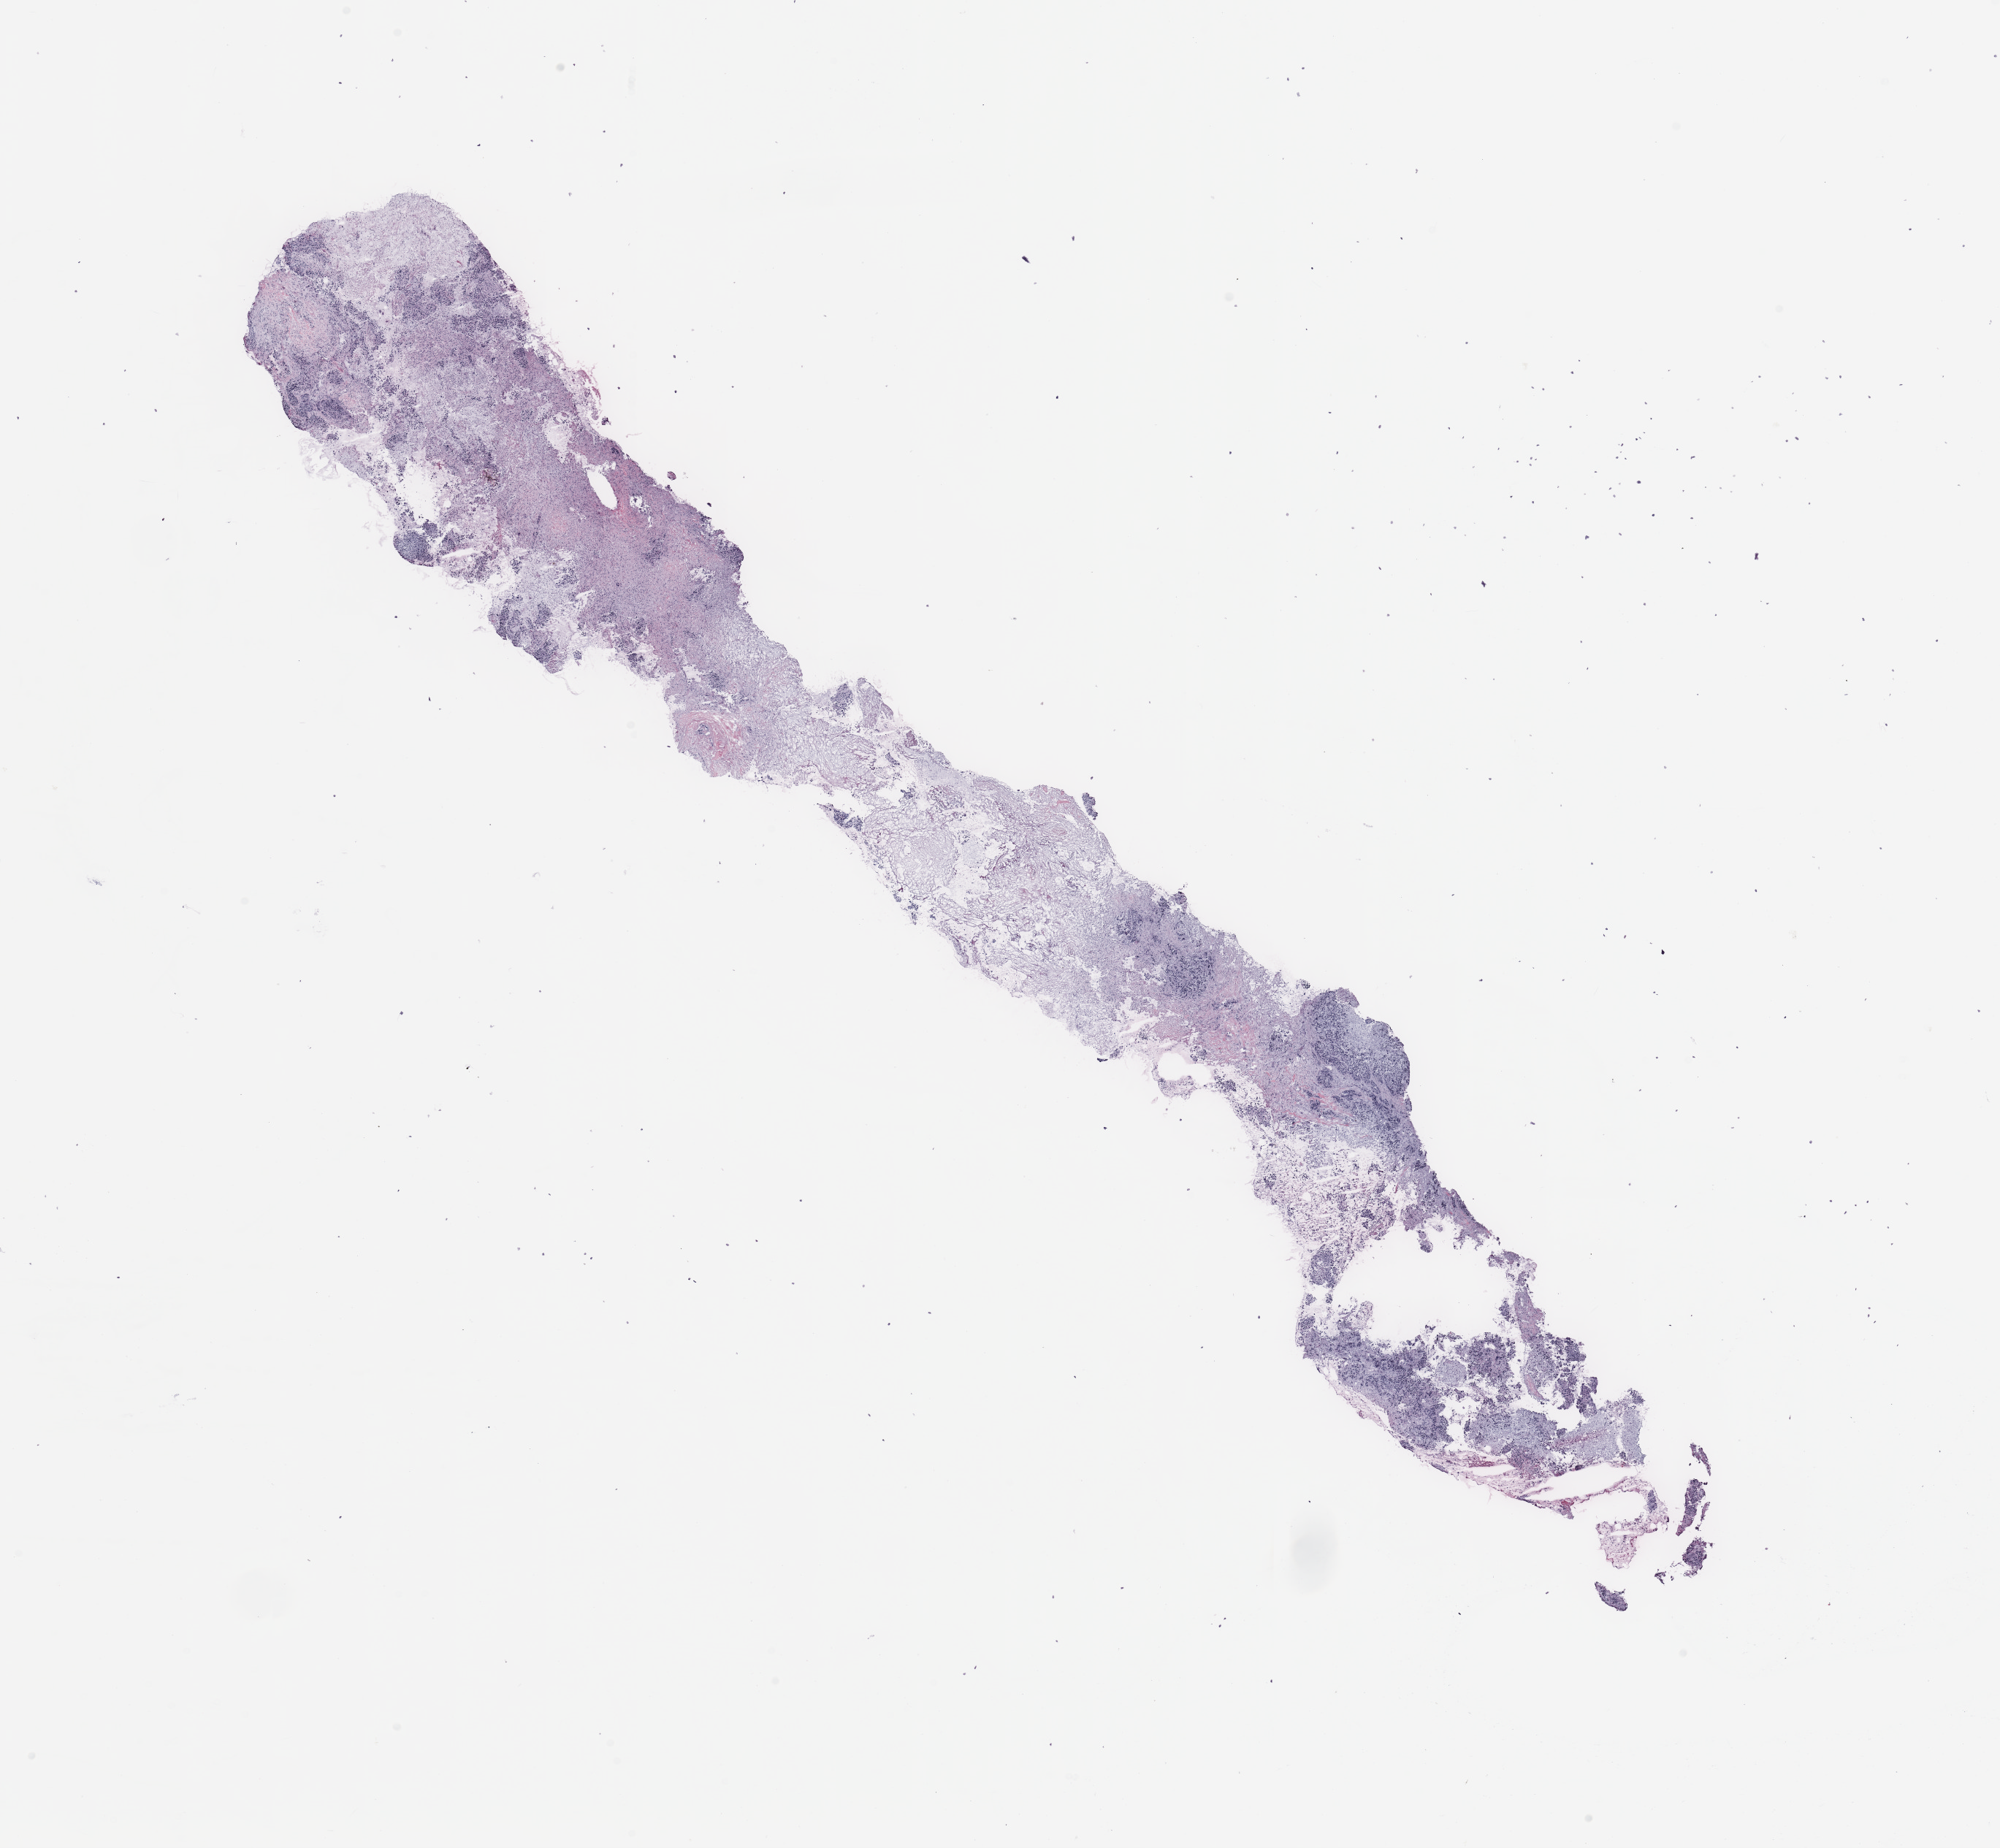
Digitized H&E tissue section (whole slide), a low-resolution overview of the entire scanned area, about 21.7 x 20.0 mm (from a 20x scan).
• specimen: breast, tissue type not recorded